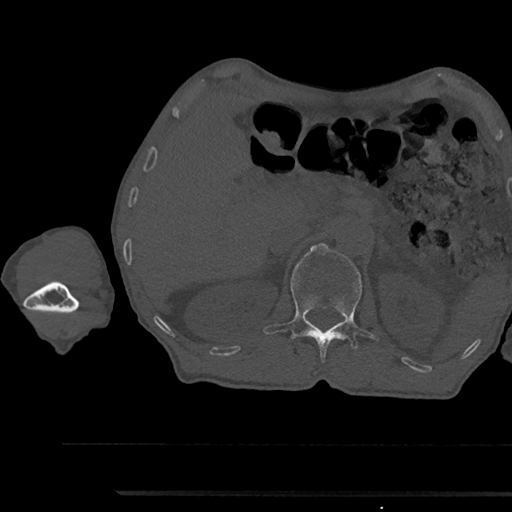
CT including the spine, one axial slice. Reconstruction kernel Br40s/3. Bone window (W 1800 / L 400 HU). 0.5 mm slice thickness. 512 × 512 image matrix. Patient: male, 79 years. From the clinical record (not read from this slice): primary cancer: prostate.
Structures marked on this image (semi-automatically segmented with operator editing):
- L1 vertebra: box from (x=264, y=243) to (x=371, y=360) px